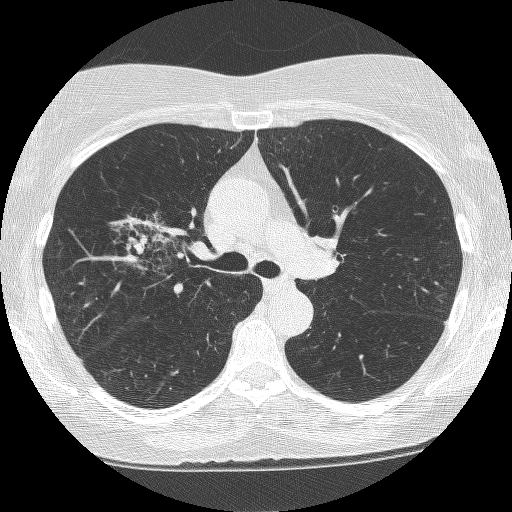
Chest CT (low-dose screening protocol), one axial image; second annual screen; lung window (W 1500 / L -600 HU); 1.25 mm slice thickness; lung (sharp) reconstruction kernel (BONE); 512 × 512 image matrix, field of view 308 × 308 mm. Female participant, aged 64 years at enrolment.
Expert-annotated lung lesion, bounding box <115,205,208,292> (left, top, right, bottom; pixels). The screening reader recorded 4 non-calcified nodules or masses ≥4 mm on this exam (right upper lobe, right upper lobe, right upper lobe, left upper lobe); which of them this box marks is not recorded. Official screen result: positive, other. Later outcome: lung cancer diagnosed 381 days after this screen (after the third annual screen) — adenocarcinoma, NOS, right upper lobe, right middle lobe, right hilum, stage IV (AJCC 6th edition), 85 mm at pathology.